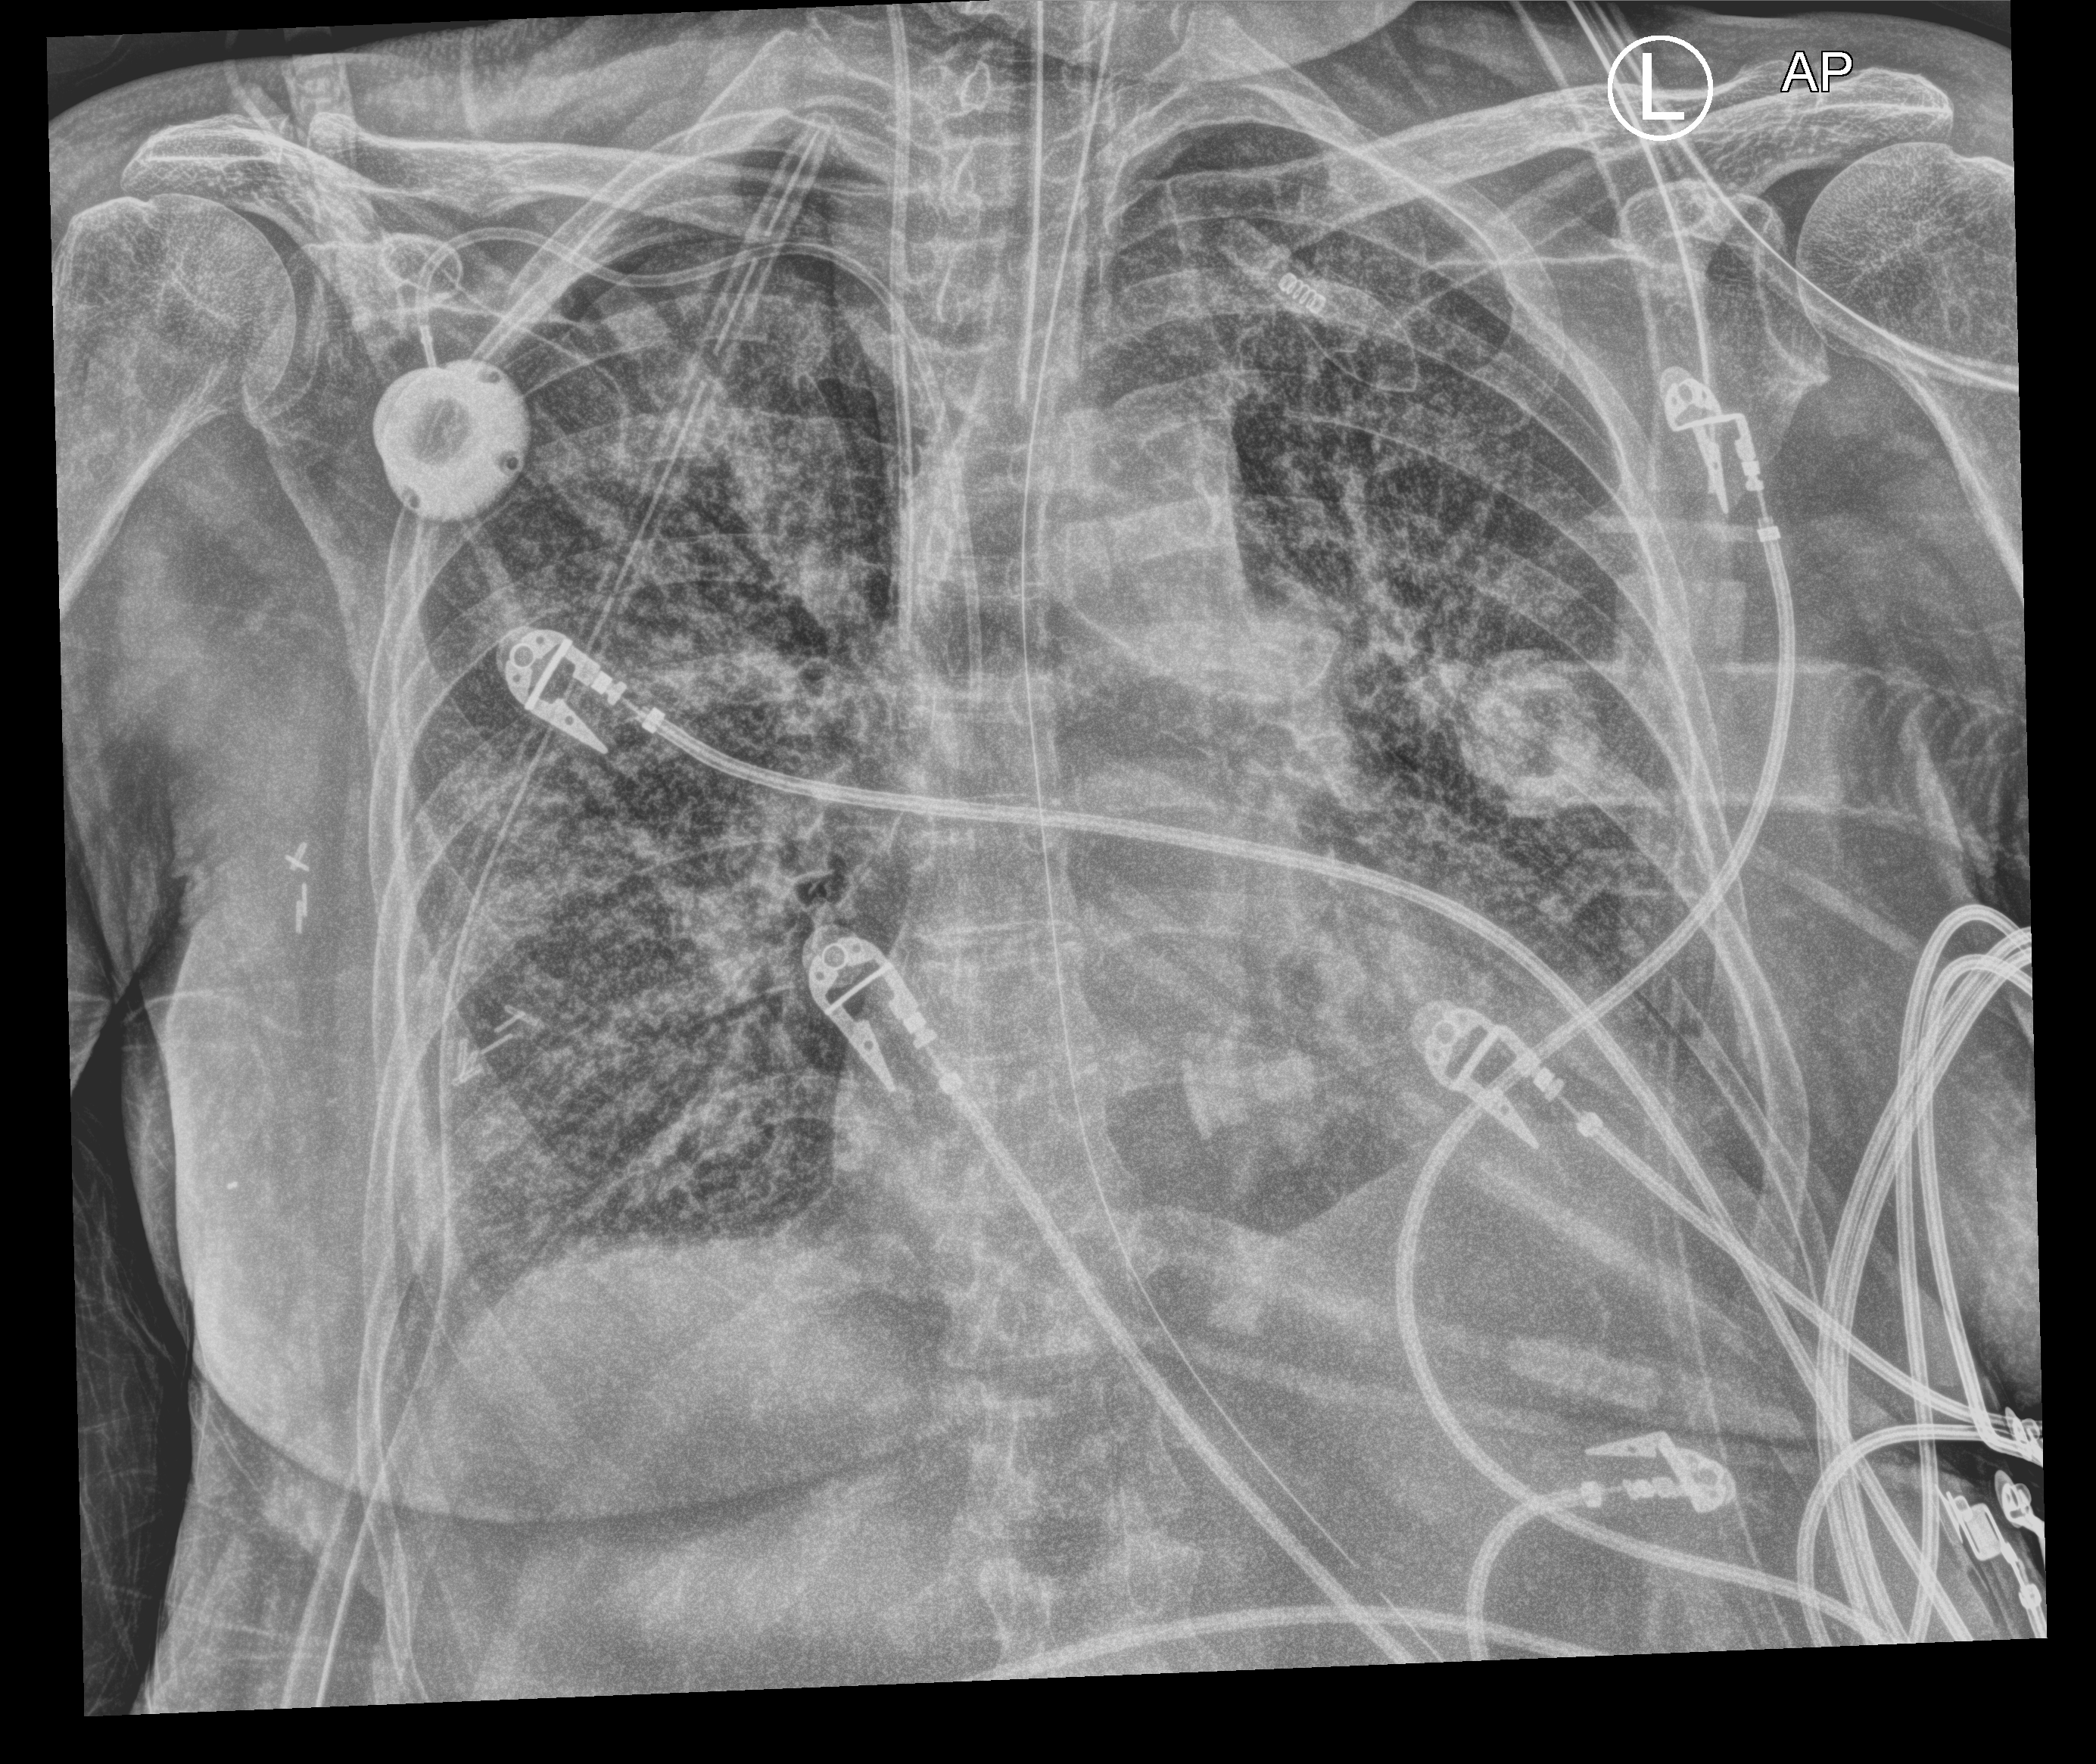
Bedside chest radiograph (computed radiography), anteroposterior (AP) projection. Female patient hospitalised with COVID-19, age 60–74 years.
From the hospital-stay record, not from the radiograph (when in the stay this image was taken is not recorded): COPD (admission record): no.